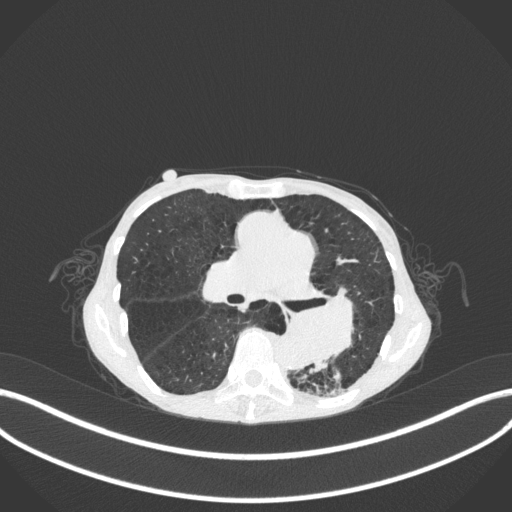
Chest CT, one axial slice; slice 156 of 347 in the series (ordered by position); reconstruction kernel B31f; 120 kVp; lung window (W 1500 / L -600 HU); 512 × 512 image matrix, field of view 400 × 400 mm. Patient: female, 70 years. Case-level facts recorded for this patient, not image findings: clinical TNM (as recorded): T3 N0 M0; histopathological grade: G3.
Outlined on this slice (rectangle marked by the reading radiologist):
- lung tumour (recorded histology: small cell carcinoma): bounding box [x1, y1, x2, y2] px = [283, 285, 363, 370]